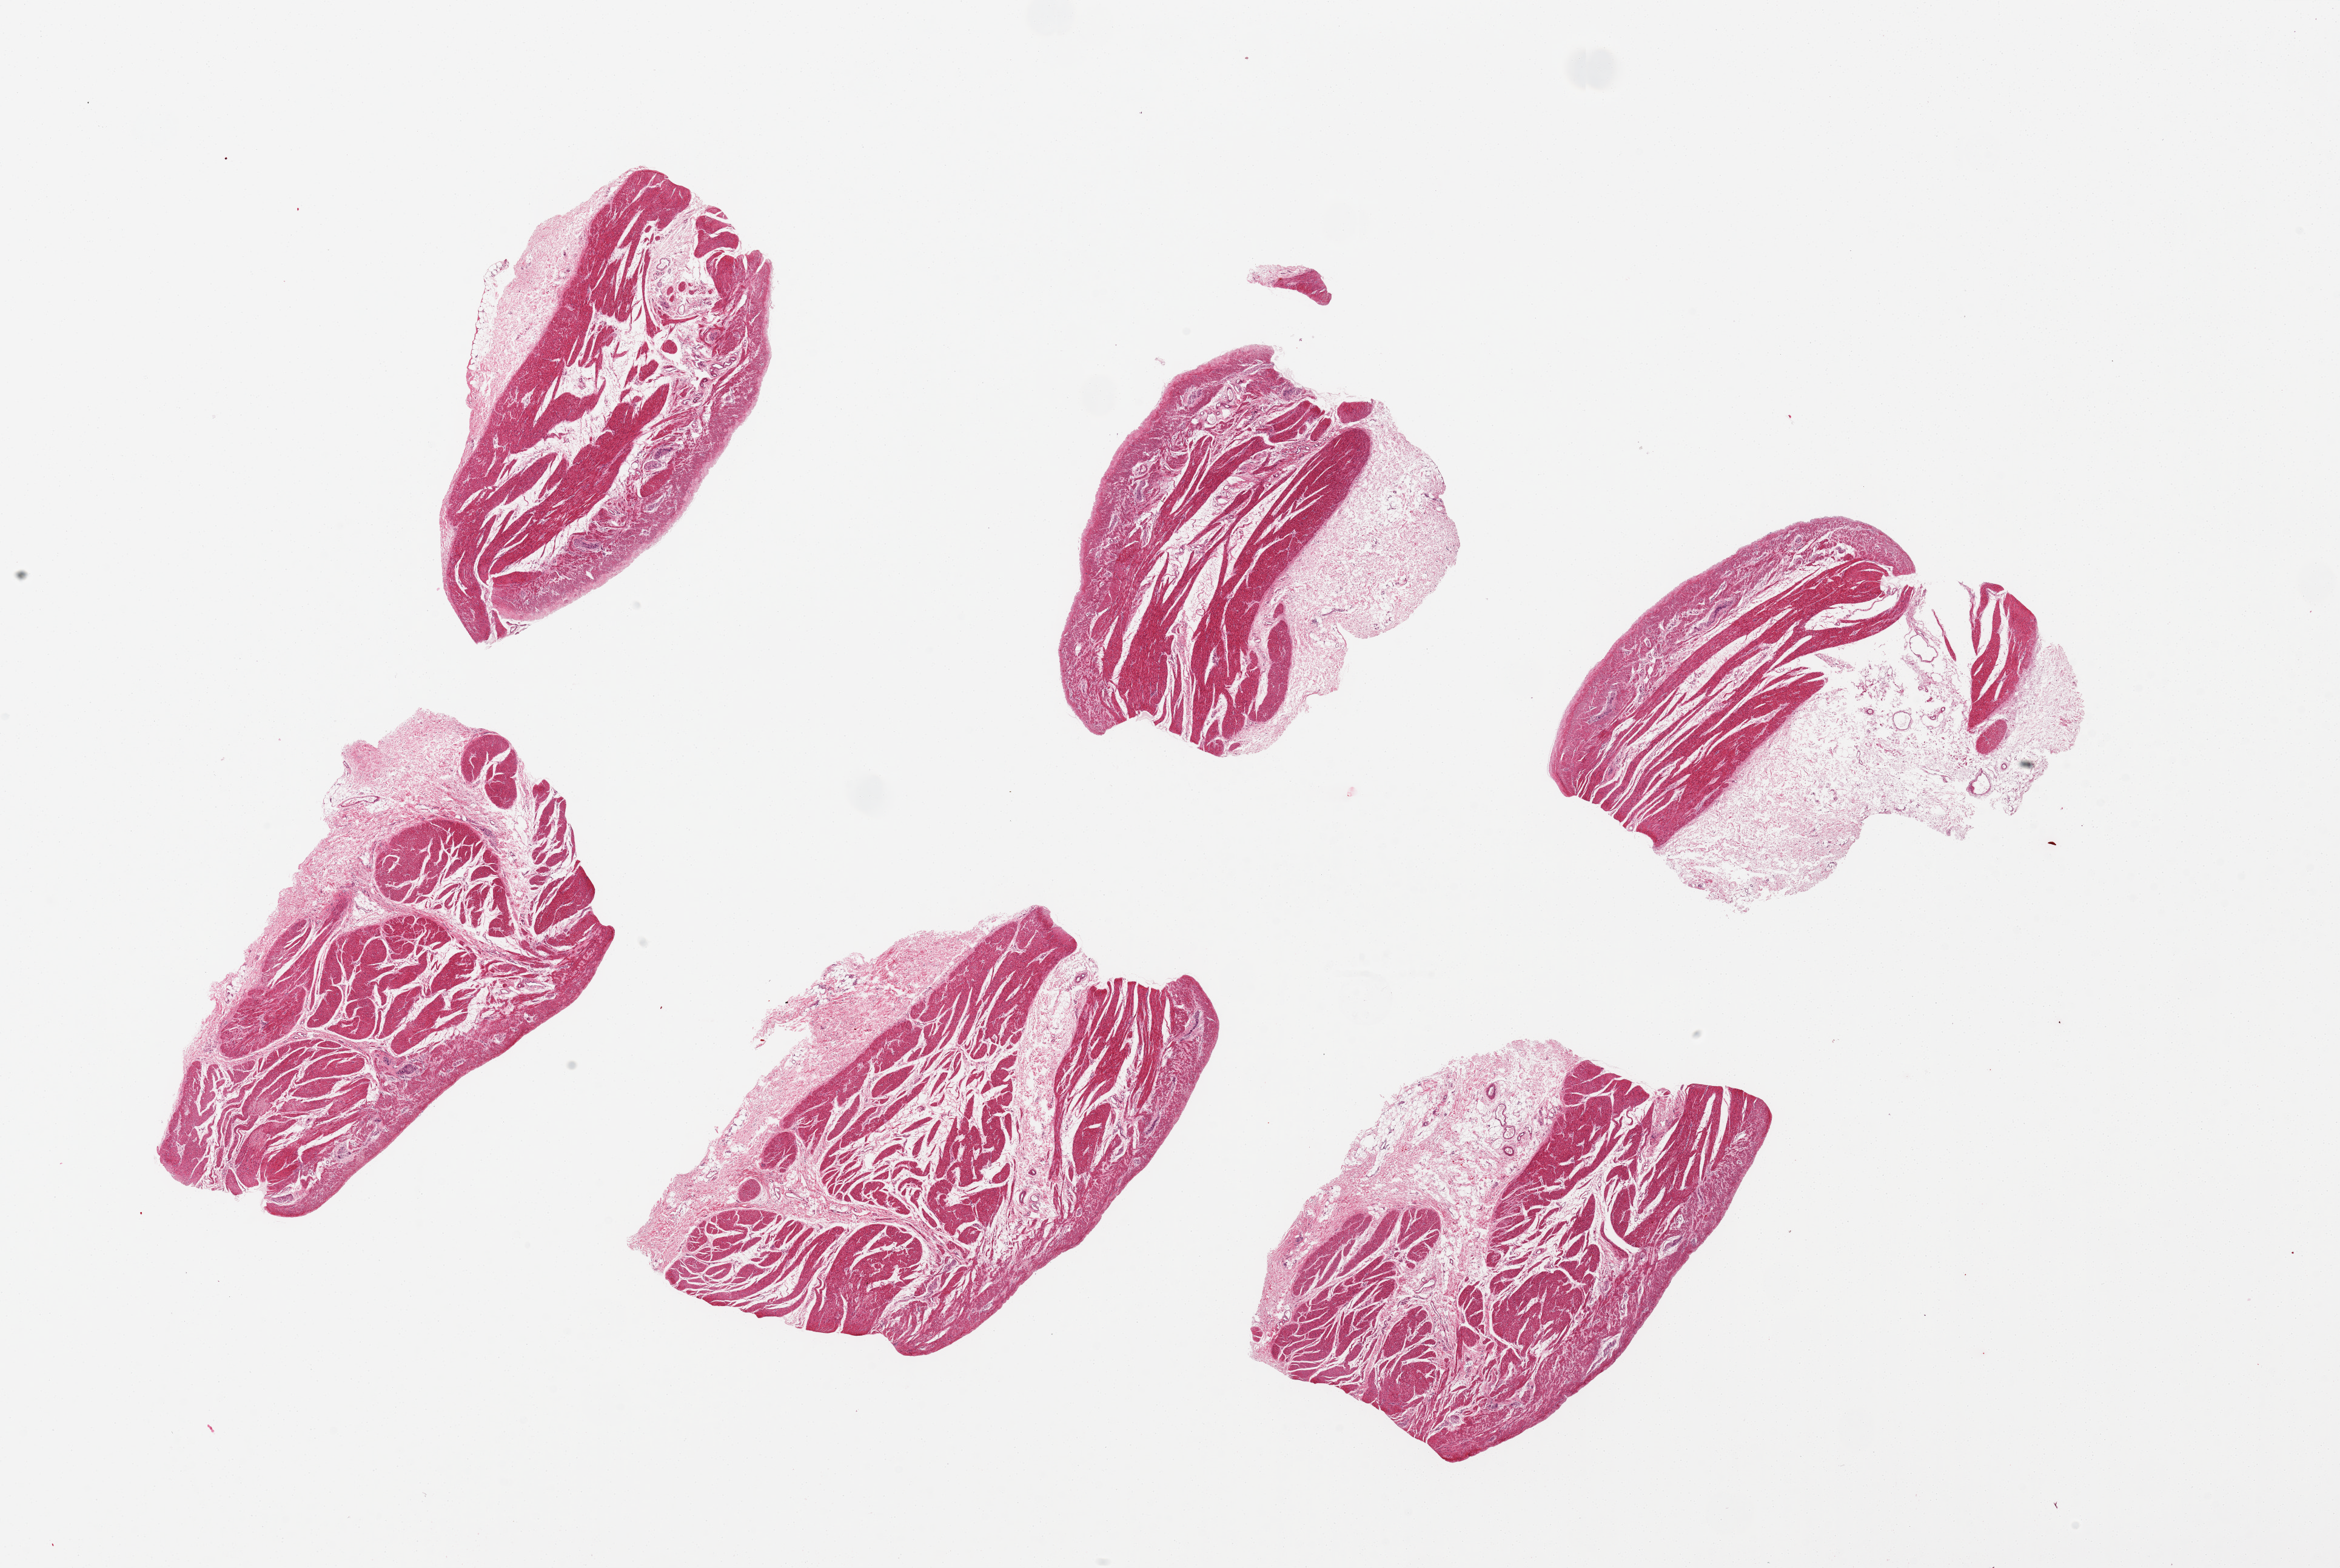
Digitized hematoxylin and eosin (H&E)-stained section, a low-resolution overview of the entire scanned area, about 30.5 x 20.5 mm; PAXgene-fixed, paraffin-embedded tissue; section of stomach (target tissue); donor tissue sample. Donor: male.
Reviewer comment on this tissue sample: 6 pieces; muscle only, no mucosa present.